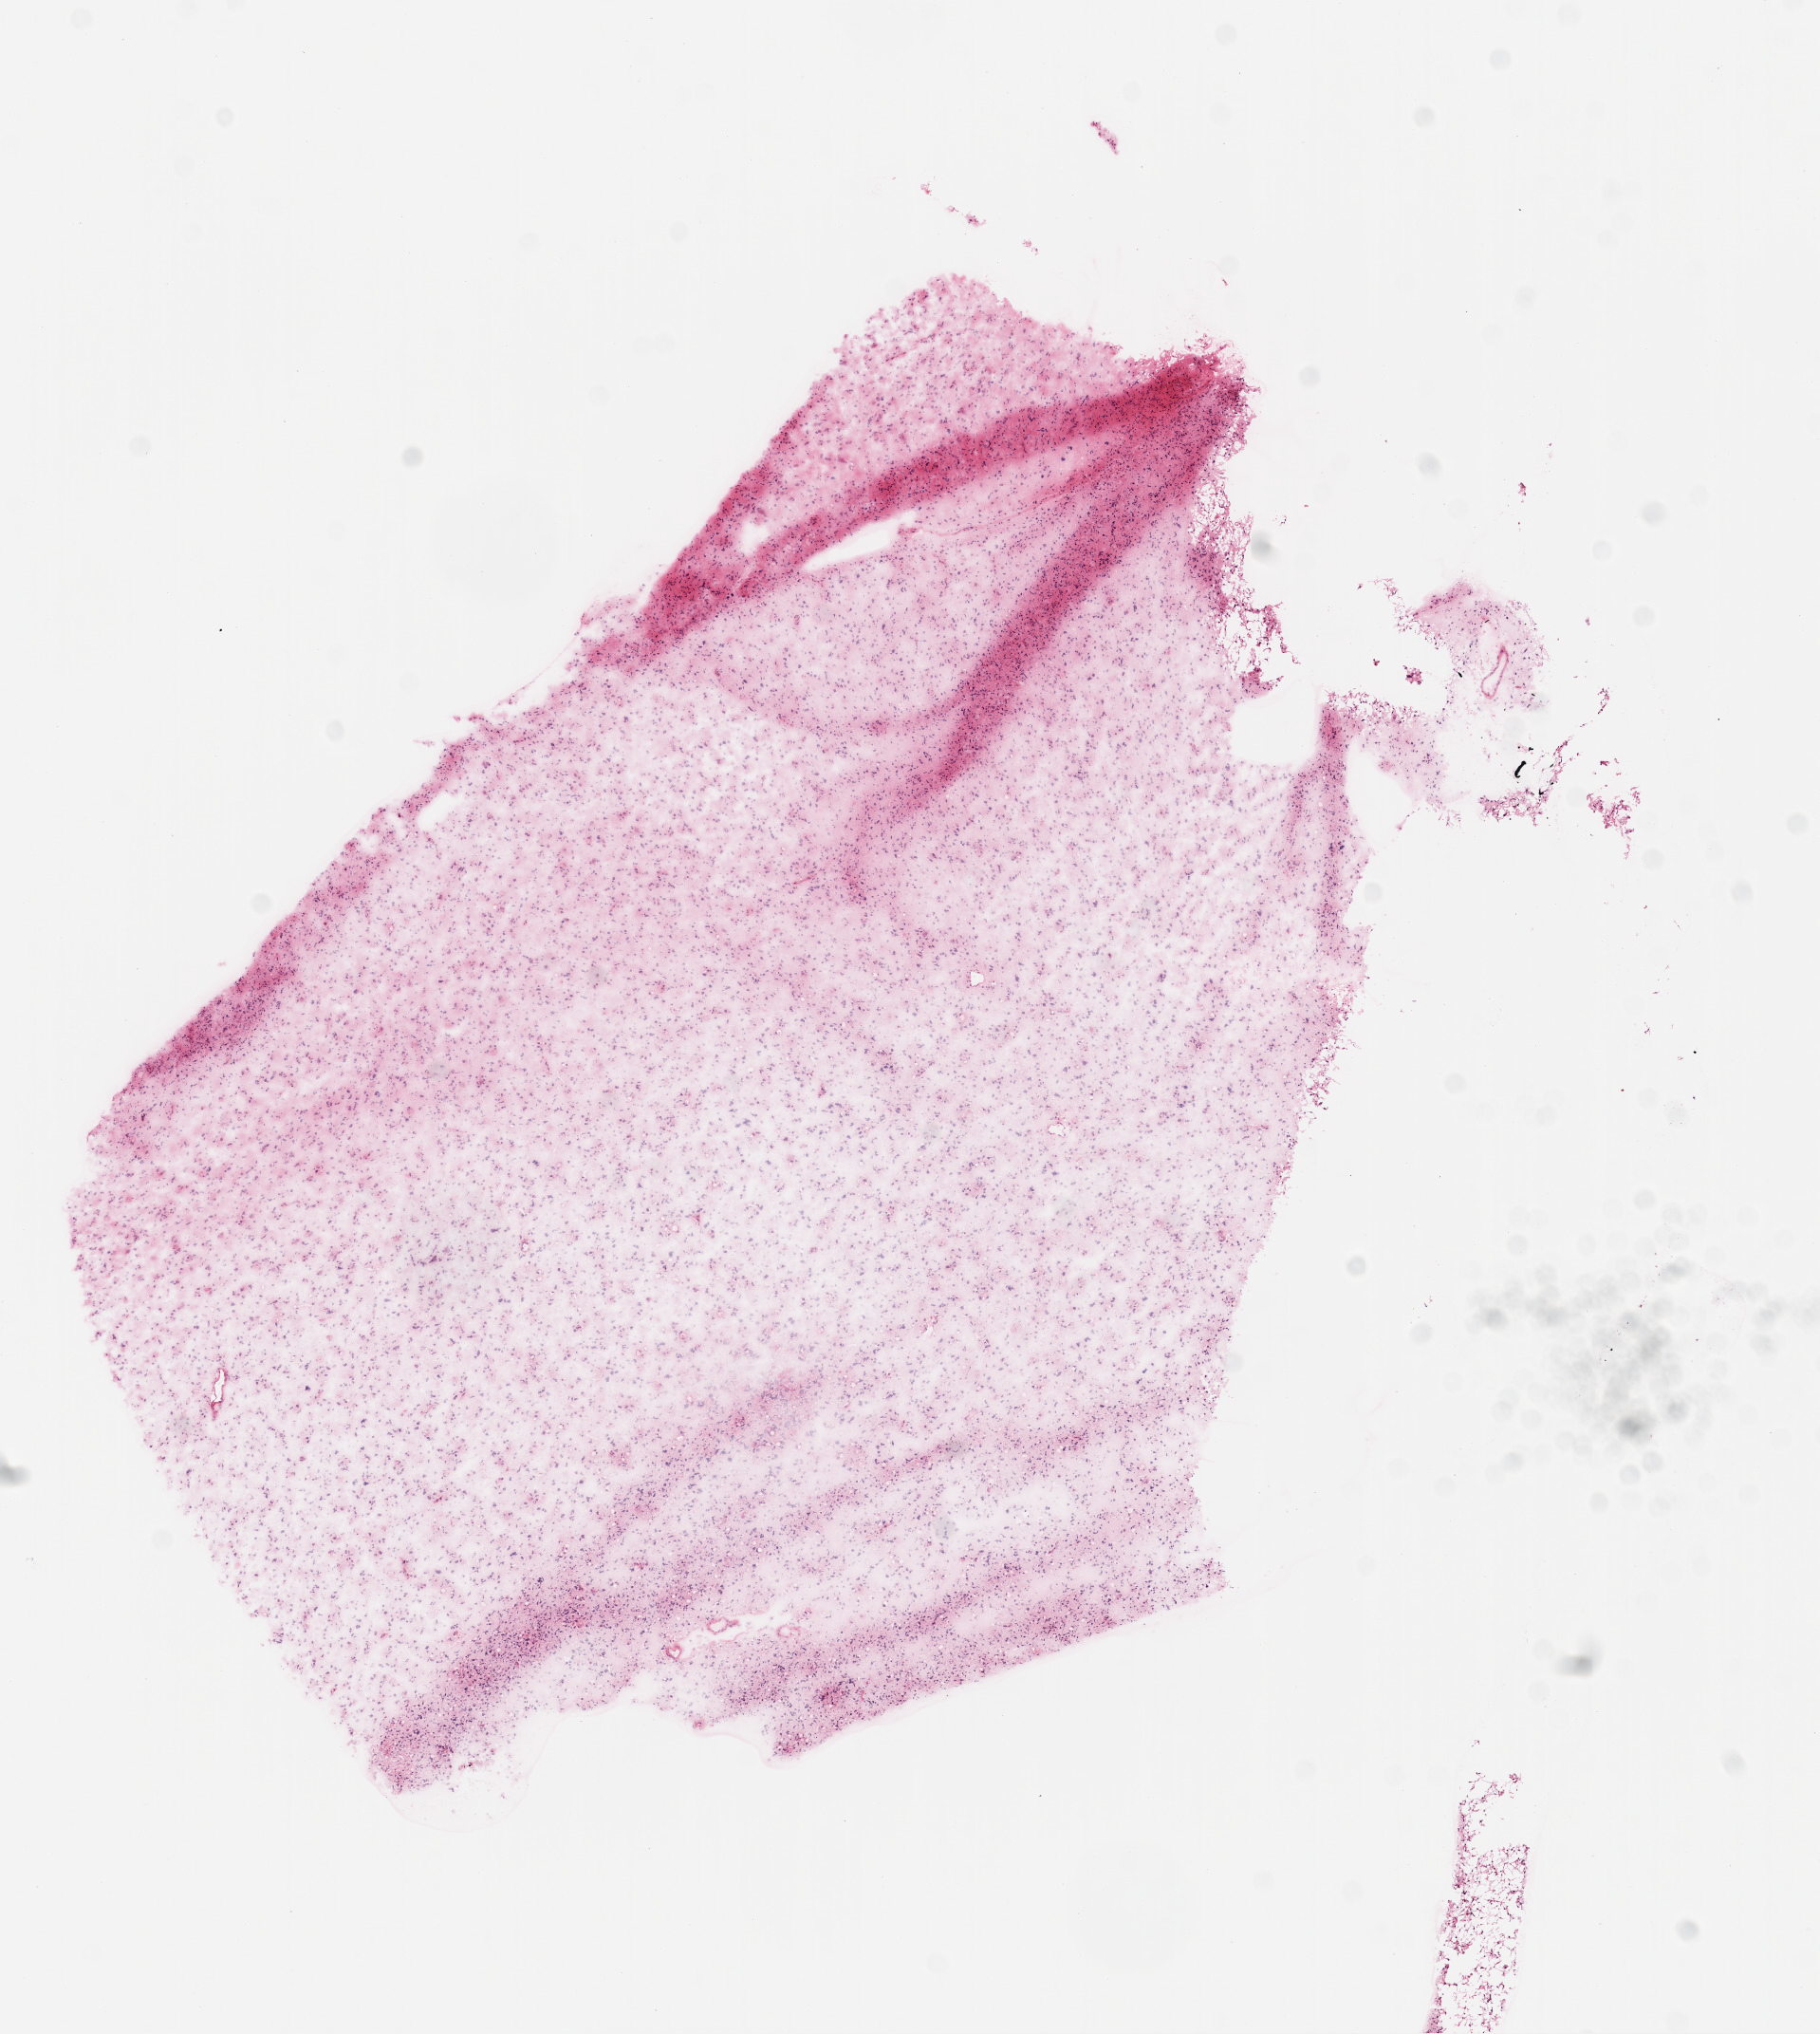
Digitized Hematoxylin and eosin (H&E) stained tissue section (whole slide), whole scanned area (about 7.7 x 8.6 mm, acquisition: 20x scan) shown as a low-resolution overview, frozen section from the top of the tissue portion, sample: primary tumour, brain. Male, age 40 years at initial diagnosis. Slide review estimates, as recorded: tumour cells 90%, tumour nuclei 80%, normal cells 0%, stromal cells 10%, necrosis 0%.
Pathologic diagnosis: Glioblastoma.